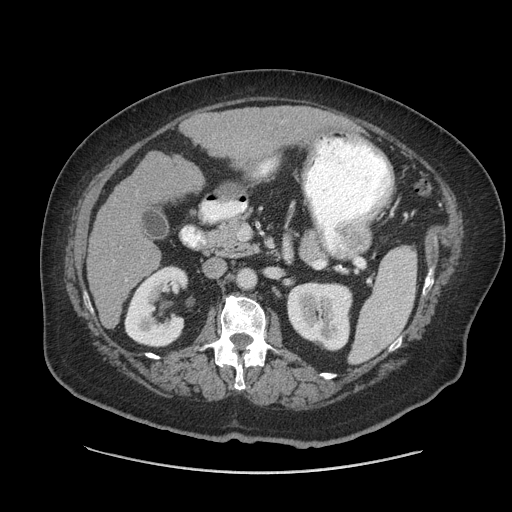
Contrast-enhanced abdominal CT (liver protocol), one axial slice; slice 28 of 91 in the series (ordered by position); reconstruction kernel STANDARD; 140 kVp; soft-tissue window (W 400 / L 40 HU); 2.5 mm slice thickness; 512 × 512 image matrix, field of view 420 × 420 mm. From the clinical record (not read from this slice): diagnosis: hepatocellular carcinoma (patient treated with transarterial chemoembolisation; whether this scan precedes or follows treatment is not stated here); TNM stage (as recorded): Stage-I; Child-Pugh class: A.
Outlined on this slice (semi-automatic segmentation, software-assisted and operator-edited):
- liver parenchyma outside the tumour (the mass and vessels are separate outlines, so this box may not span the whole liver): box from (x=86, y=106) to (x=345, y=328) px
- liver vessels: (x=261, y=161)–(x=272, y=174)